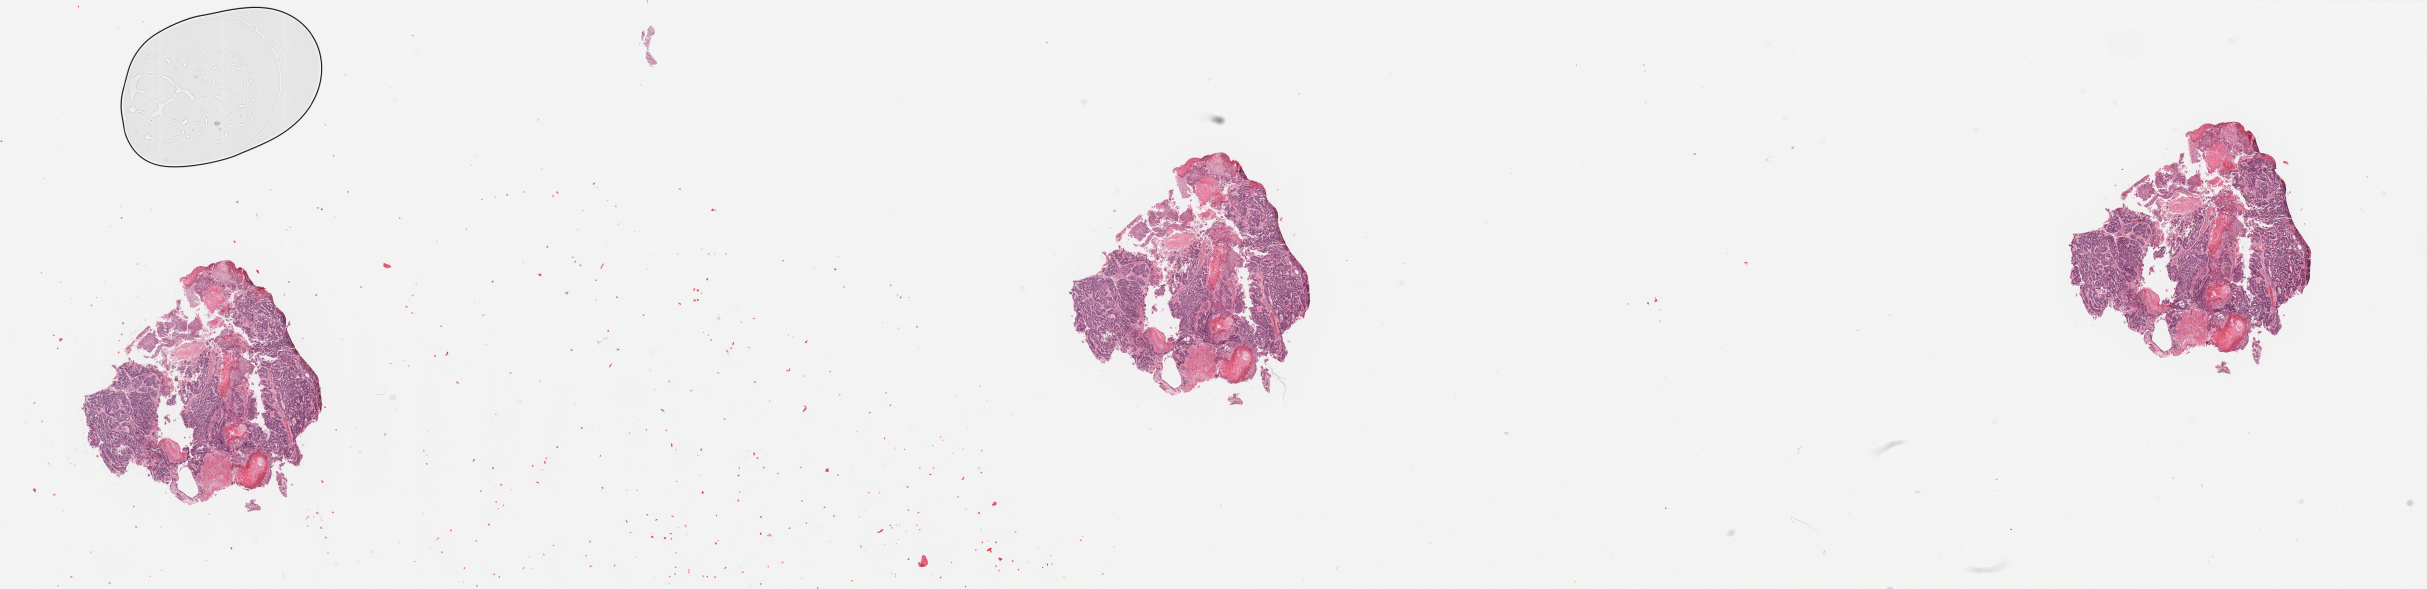
H&E whole-slide image — low-resolution overview of the scanned area, about 38.4 x 9.3 mm (from a 20x scan); tumour tissue sample, sampled site: uterus. Patient: female, age 56 years. Histologic grade: G1 (well differentiated). Pathologist review of this section (percent, as recorded): tumour nuclei 85%, necrosis 2%.
Histologic diagnosis: Endometrioid adenocarcinoma, NOS. AJCC pathologic stage: I. Primary tumour site (as recorded): anterior endometrium.